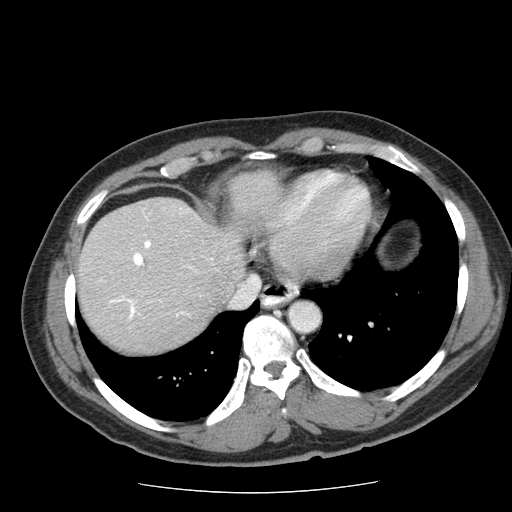
Contrast-enhanced abdominal CT (liver protocol), one axial slice. Slice 59 of 85 in the series (ordered by position). Reconstruction kernel STANDARD. 120 kVp. Soft-tissue window (W 400 / L 40 HU). 2.5 mm slice thickness. 512 × 512 image matrix, field of view 360 × 360 mm. From the clinical record (not read from this slice): diagnosis: hepatocellular carcinoma (patient treated with transarterial chemoembolisation; whether this scan precedes or follows treatment is not stated here); TNM stage (as recorded): Stage-IIIA; Child-Pugh class: A; tumour differentiation: well differentiated; tumour nodularity: multinodular.
Outlined on this slice (semi-automatic segmentation, software-assisted and operator-edited):
- liver parenchyma outside the tumour (the mass and vessels are separate outlines, so this box may not span the whole liver): bounding box [x1, y1, x2, y2] px = [76, 172, 264, 352]
- liver vessels: [110, 240, 192, 319]